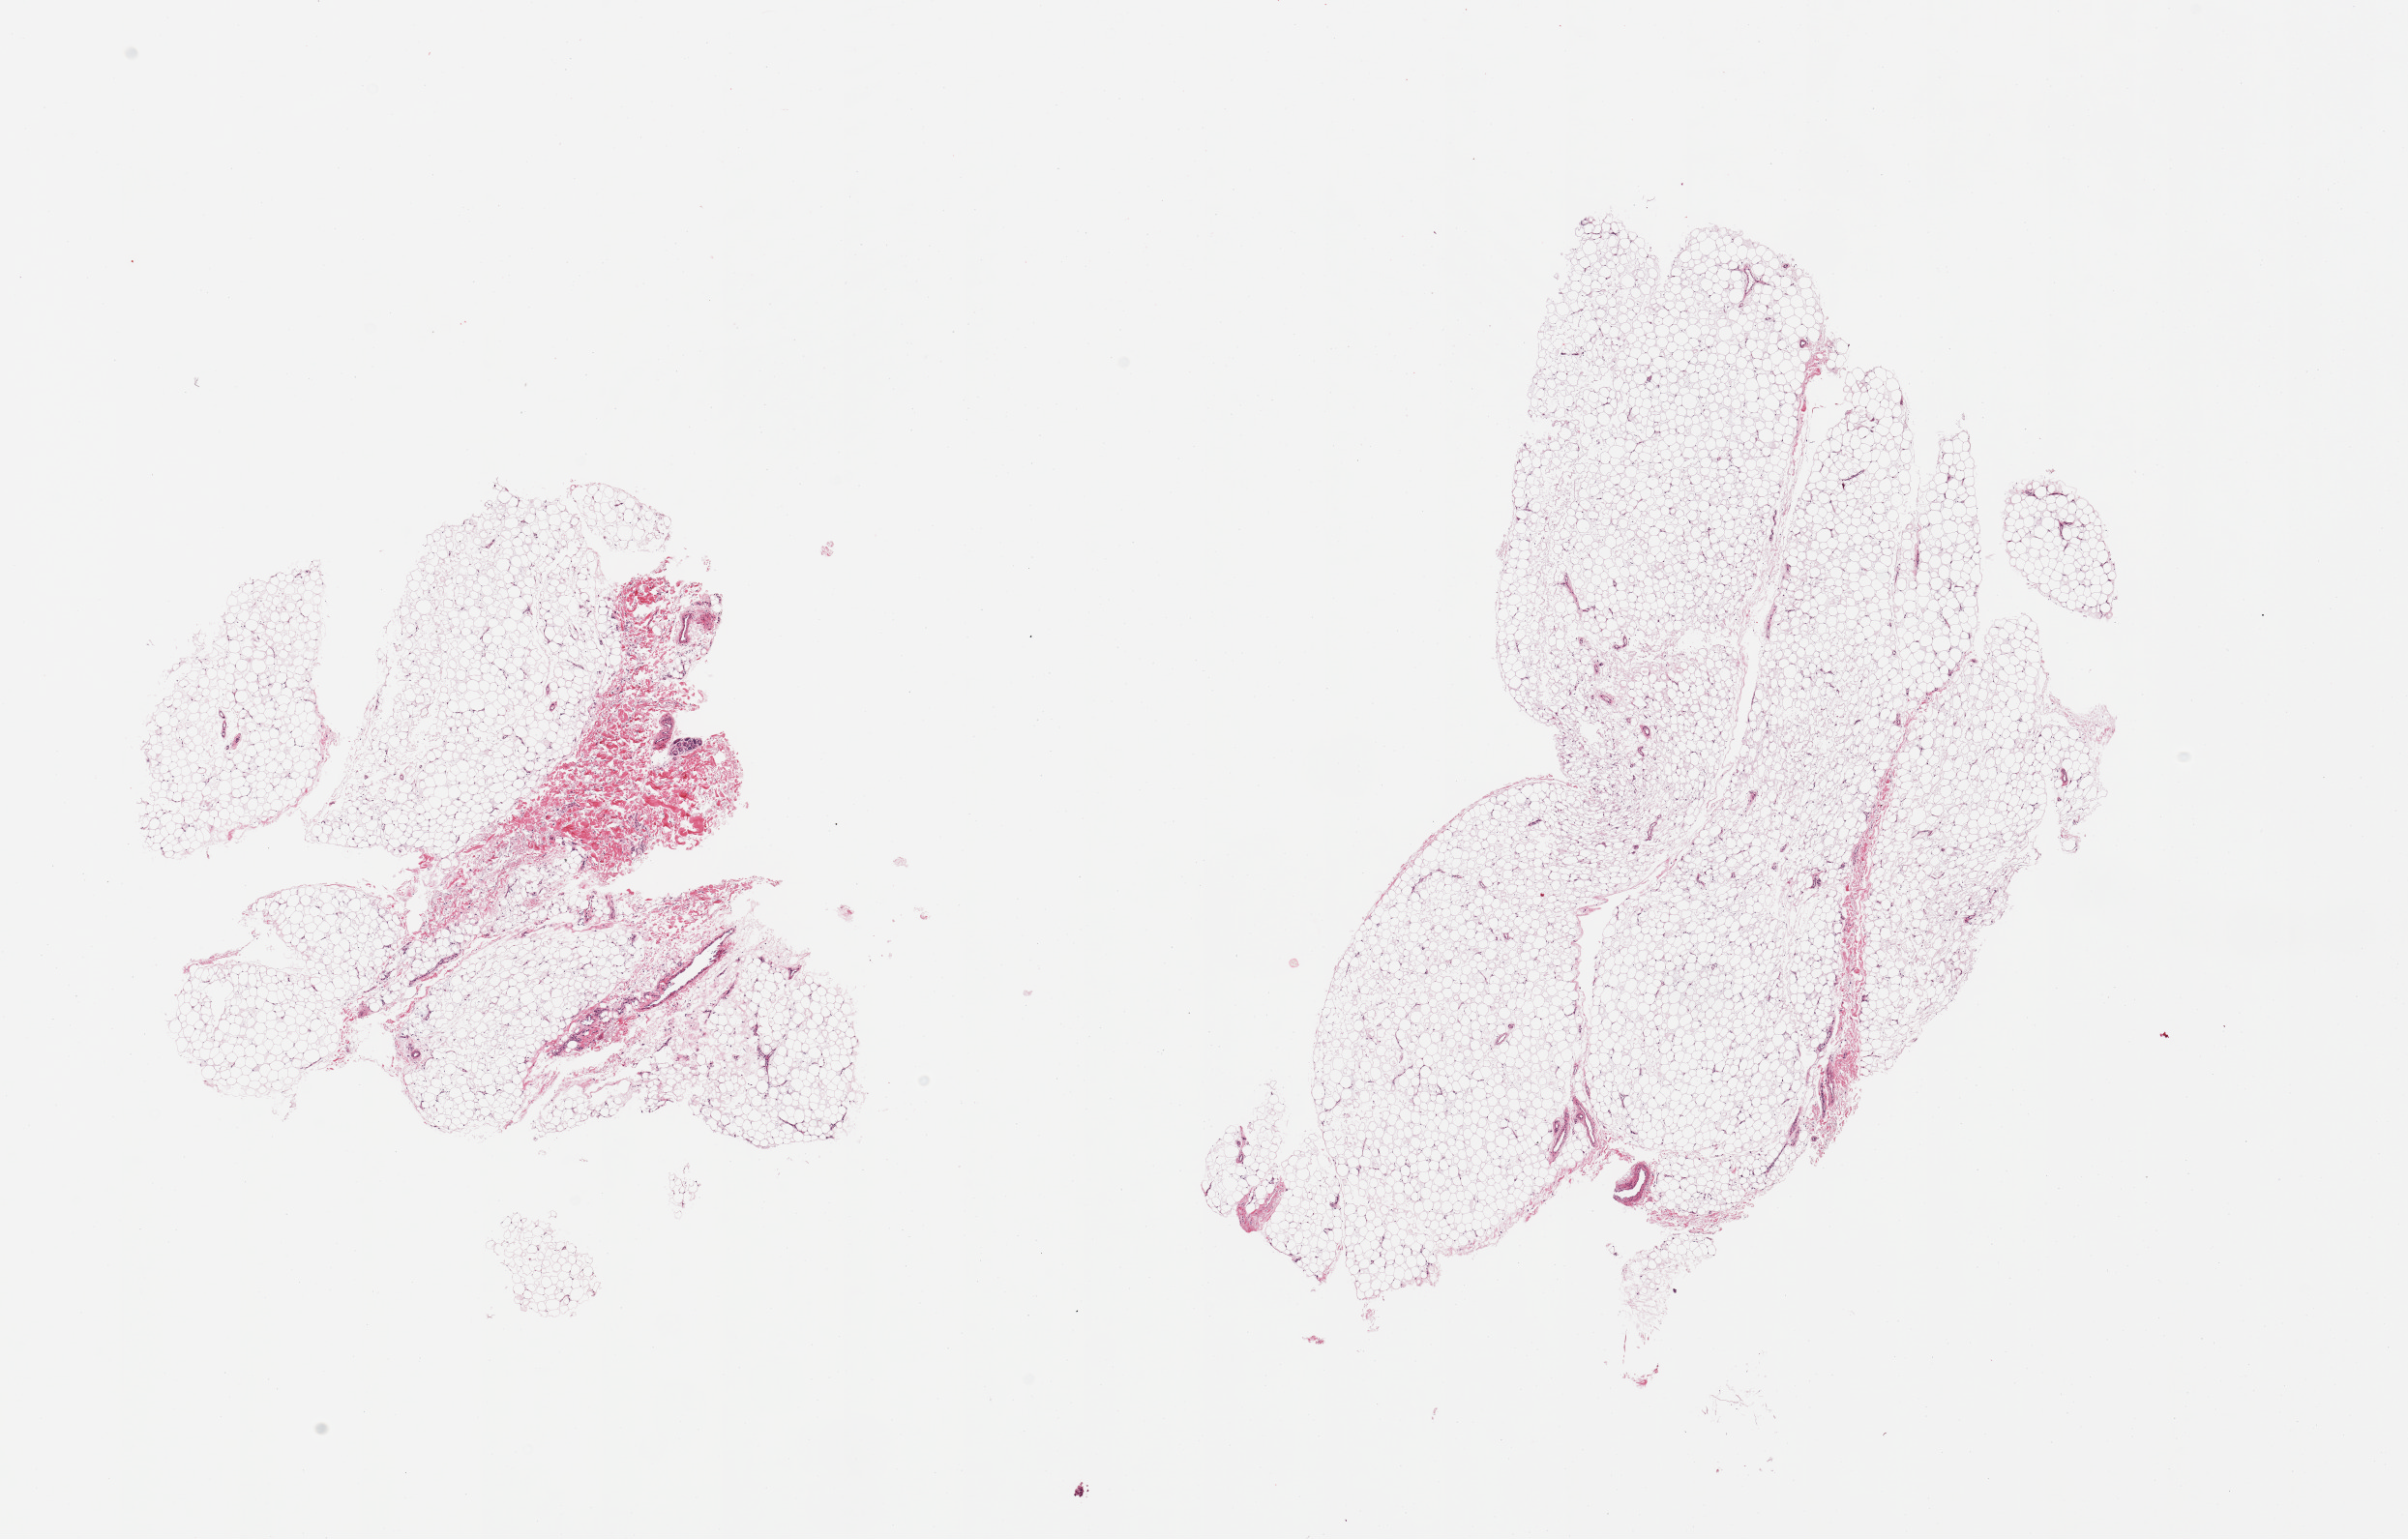
Hematoxylin and eosin (H&E) whole-slide image — low-resolution overview of the scanned area, about 19.7 x 12.6 mm (slide scanned at 20x). PAXgene-fixed paraffin-embedded (PFPE) section. Section of adipose tissue (target tissue). Tissue donor sample. Male donor.
Reviewer comment on this tissue sample: 2 pieces; 1 piece includes few glands within fibrous tissue (~15%).